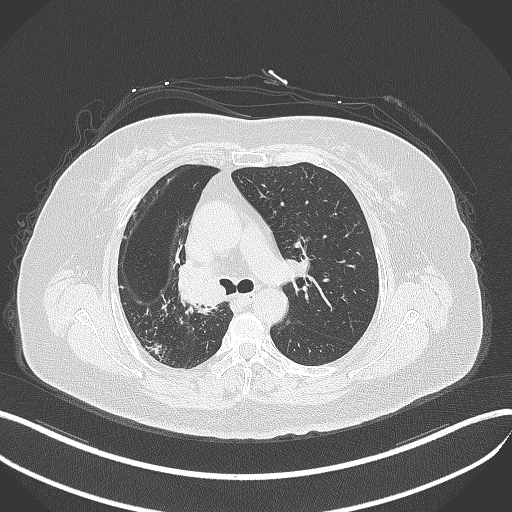
Chest CT, one axial slice; position 233 of 376 along the scan axis; reconstruction kernel B70f; 120 kVp; lung window (W 1500 / L -600 HU); 512 × 512 image matrix, field of view 400 × 400 mm. Patient: female, 60 years. Case-level facts recorded for this patient, not image findings: clinical TNM (as recorded): T1c N0 M0; histopathological grade: G1-G2.
Outlined on this slice (bounding box drawn by a radiologist):
- lung tumour (recorded histology: squamous cell carcinoma): box from (x=177, y=261) to (x=233, y=309) px